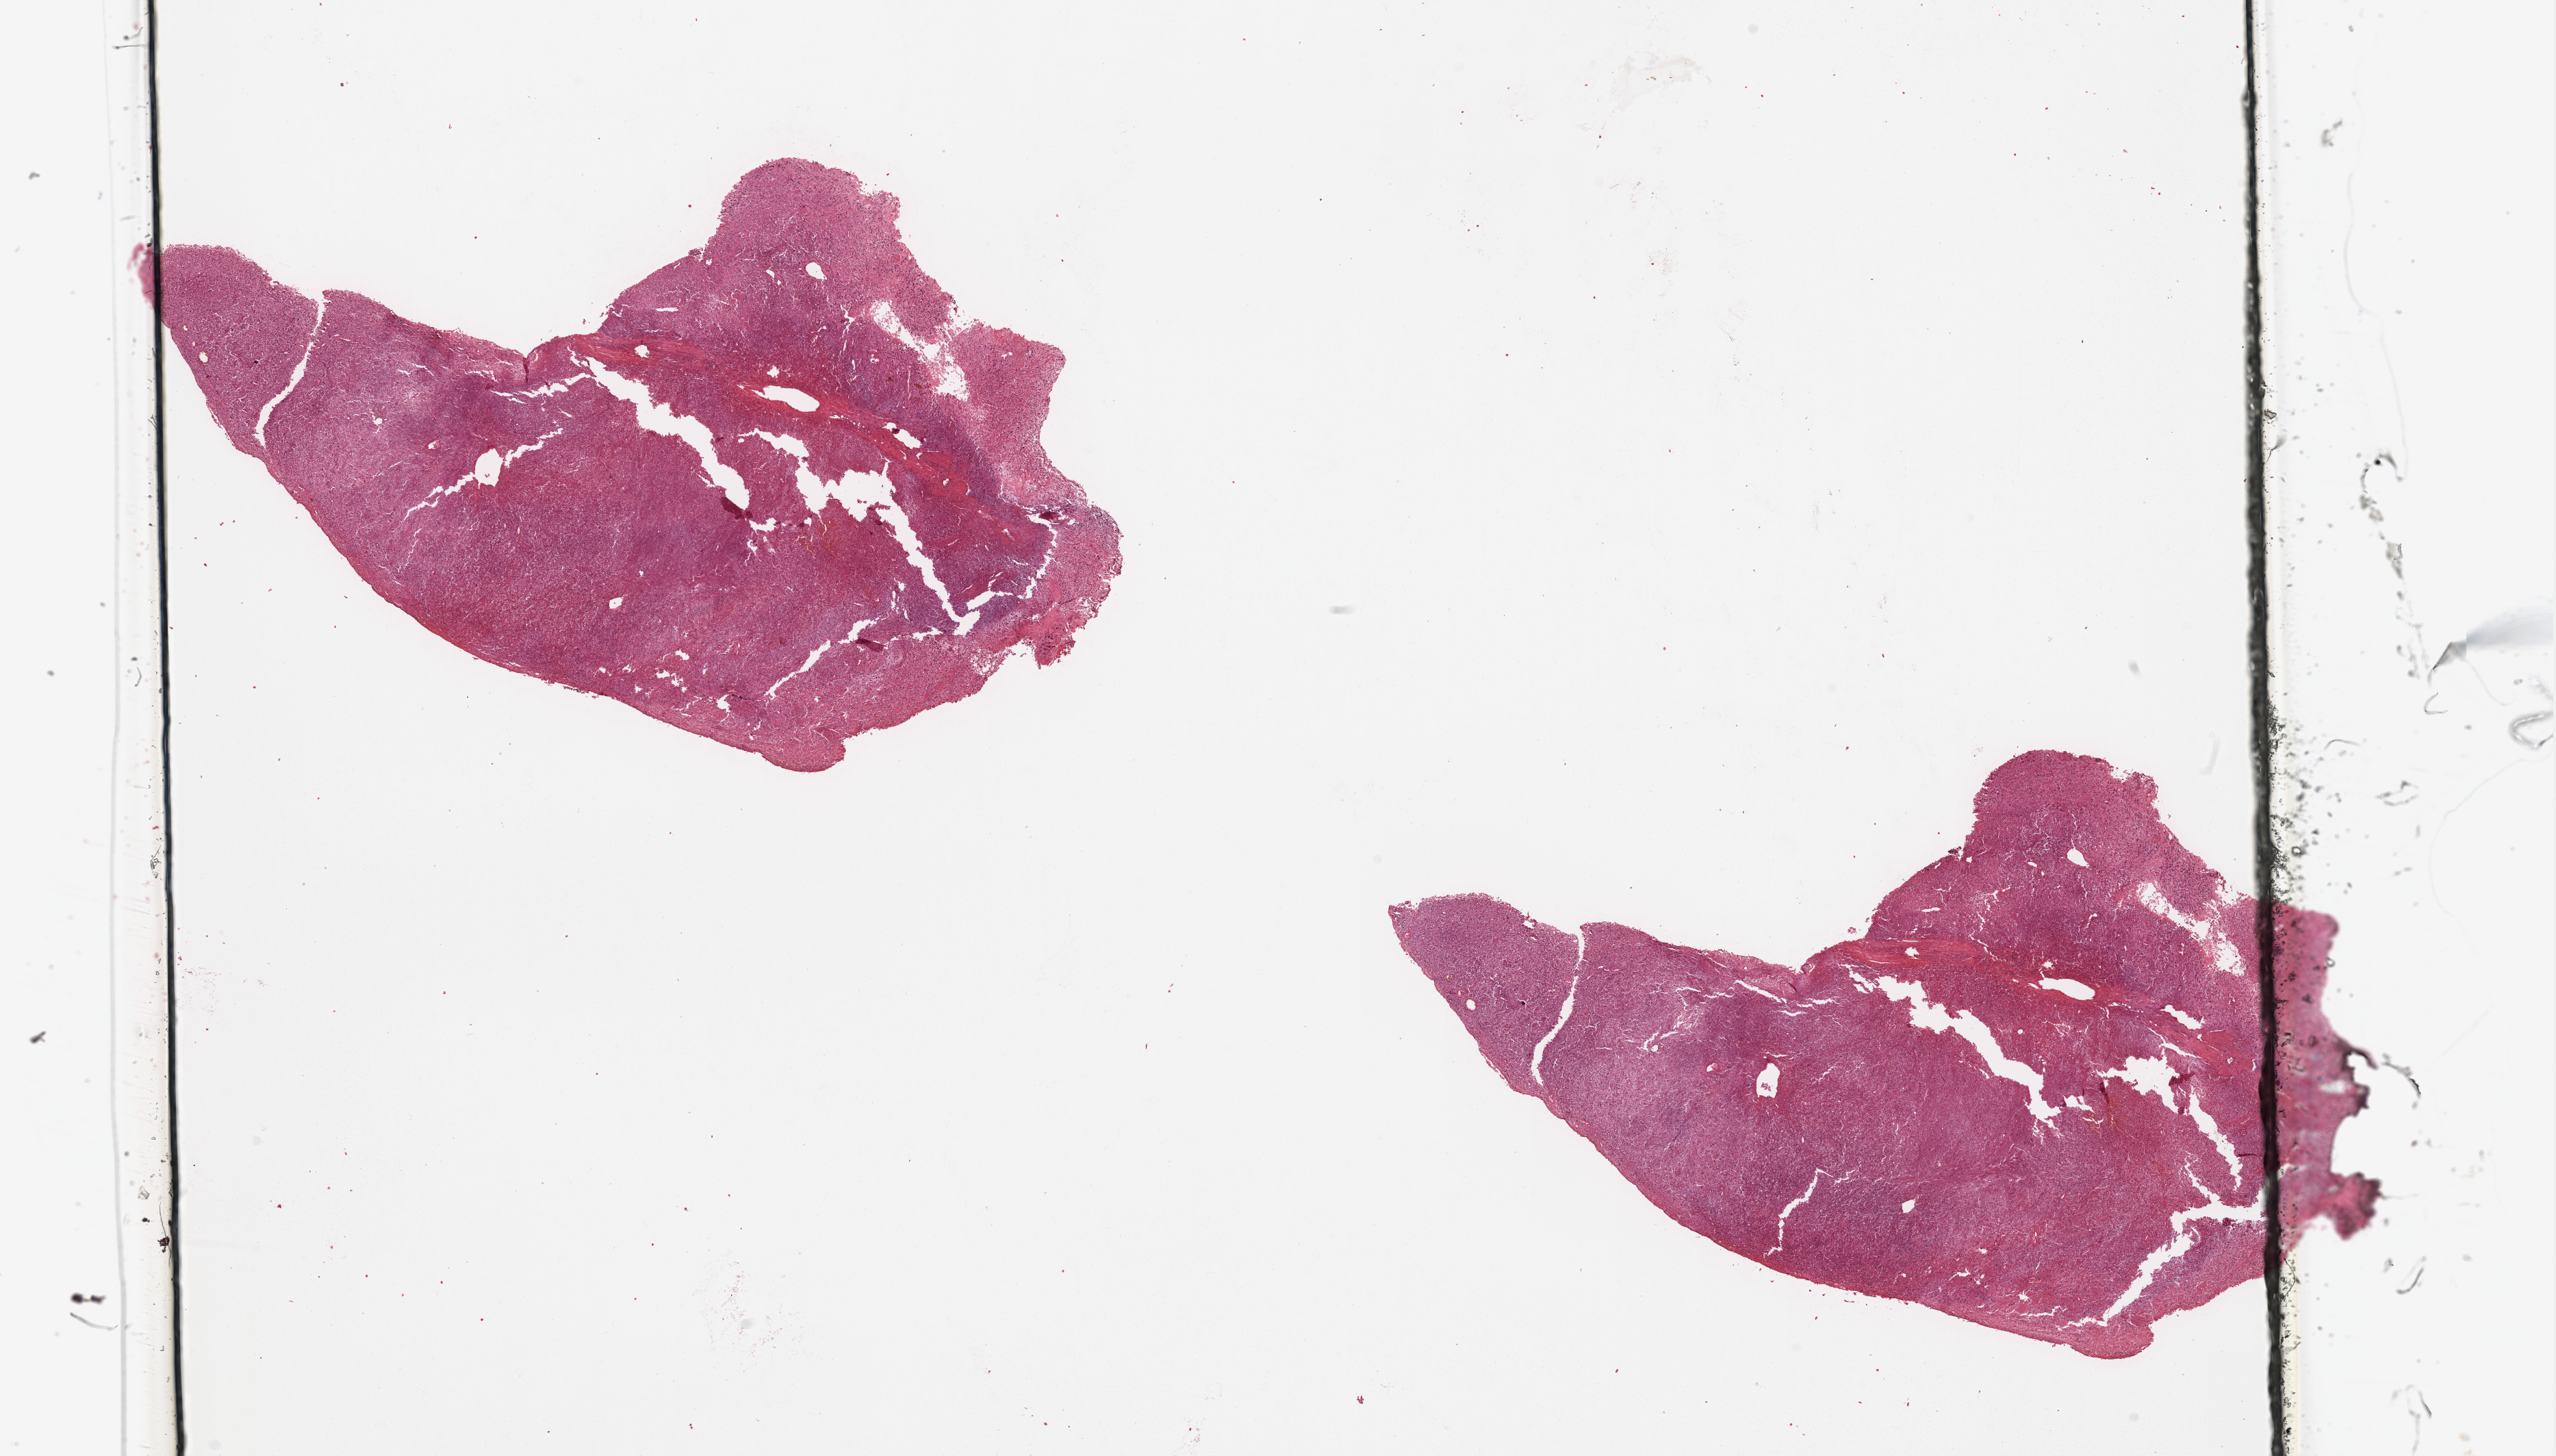
Digitized H&E tissue section (whole slide) — low-resolution overview of the scanned area, about 29.5 x 16.8 mm (from a 20x scan). 80-year-old female patient.
Patient diagnosis (cohort enrolment): sarcoma (site not recorded at cohort level). Primary tumour site (as recorded): gynecologic.